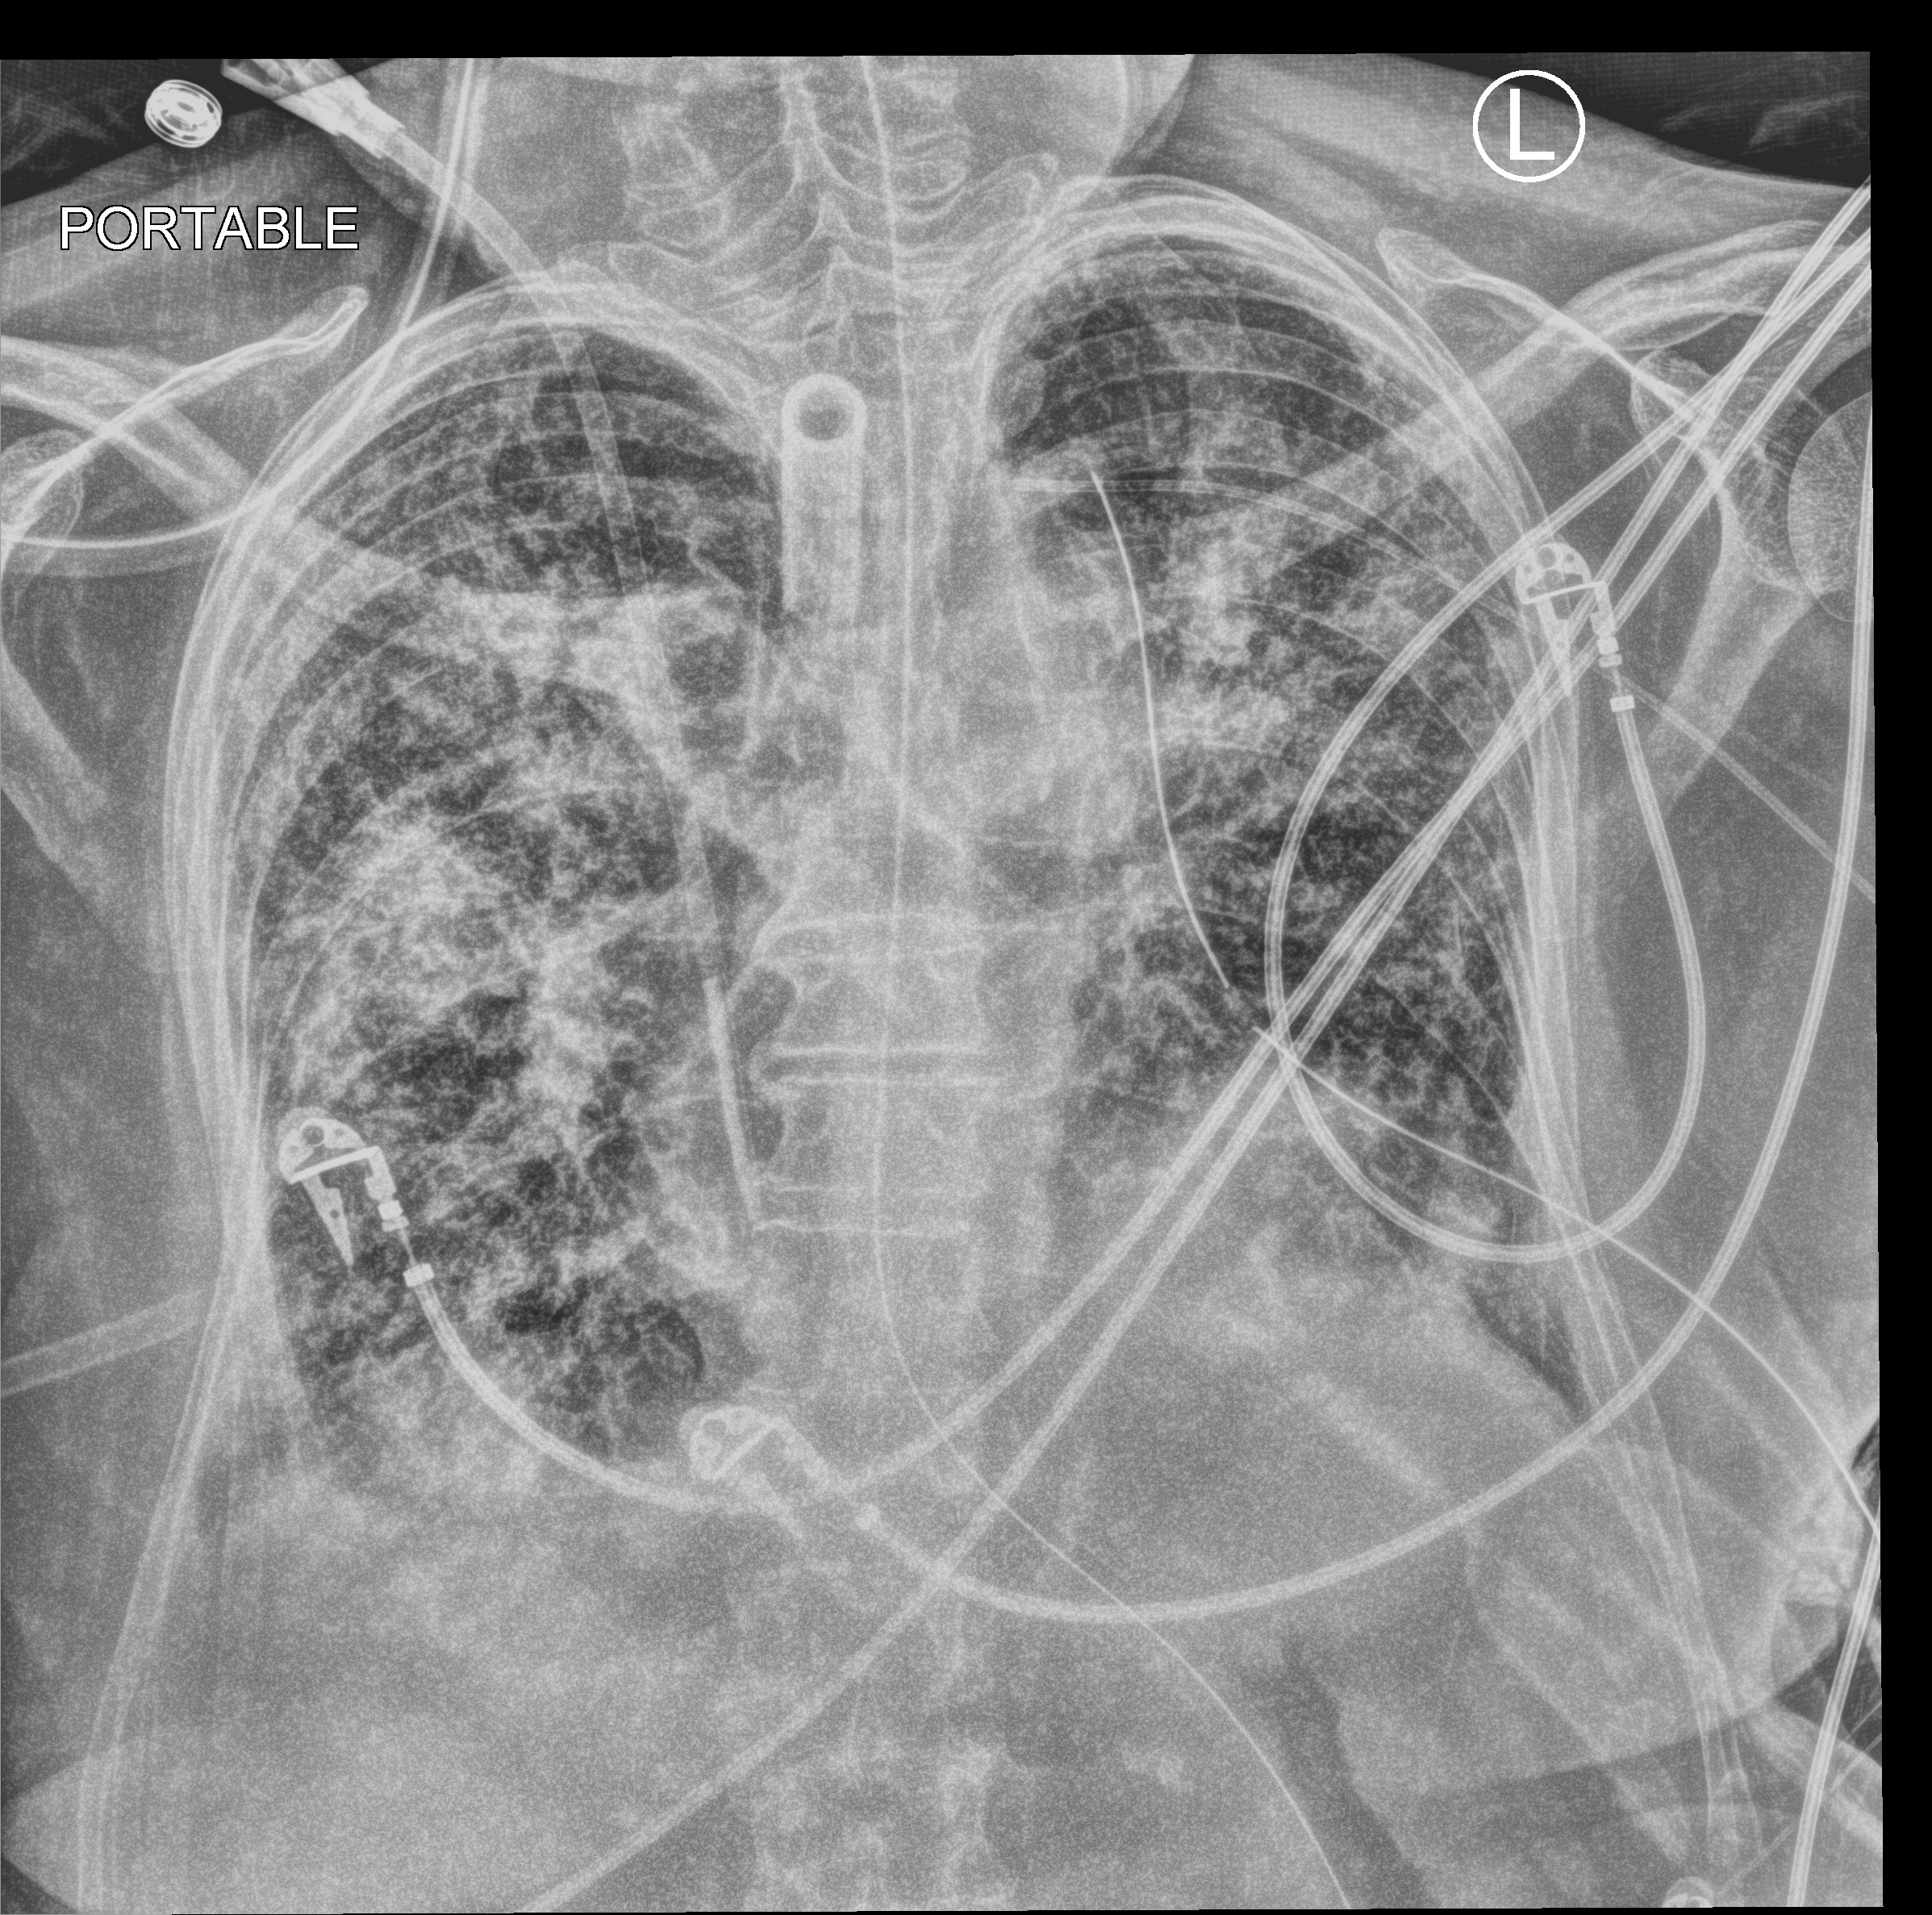
Portable chest radiograph, anteroposterior (AP) projection. Patient hospitalised with COVID-19; female, aged 75–90 years.
From the hospital-stay record, not from the radiograph (when in the stay this image was taken is not recorded): mechanically ventilated during this hospital stay: yes.